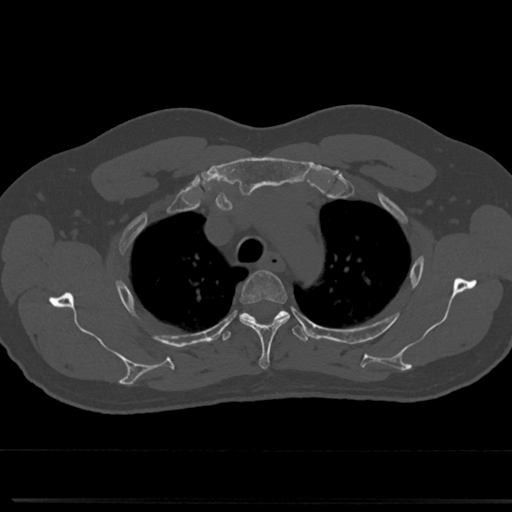
CT including the spine, one axial slice. Position 576 of 817 along the scan axis. 120 kVp. Bone window (W 1800 / L 400 HU). 0.5 mm slice thickness. 512 × 512 image matrix, field of view 355 × 355 mm. Patient: male, 61 years. From the clinical record (not read from this slice): primary cancer: prostate.
Structures marked on this image (semi-automatically segmented with operator editing):
- T3 vertebra: bounding box <238,271,289,370> (left, top, right, bottom; pixels)
- T4 vertebra: <221,308,309,344>